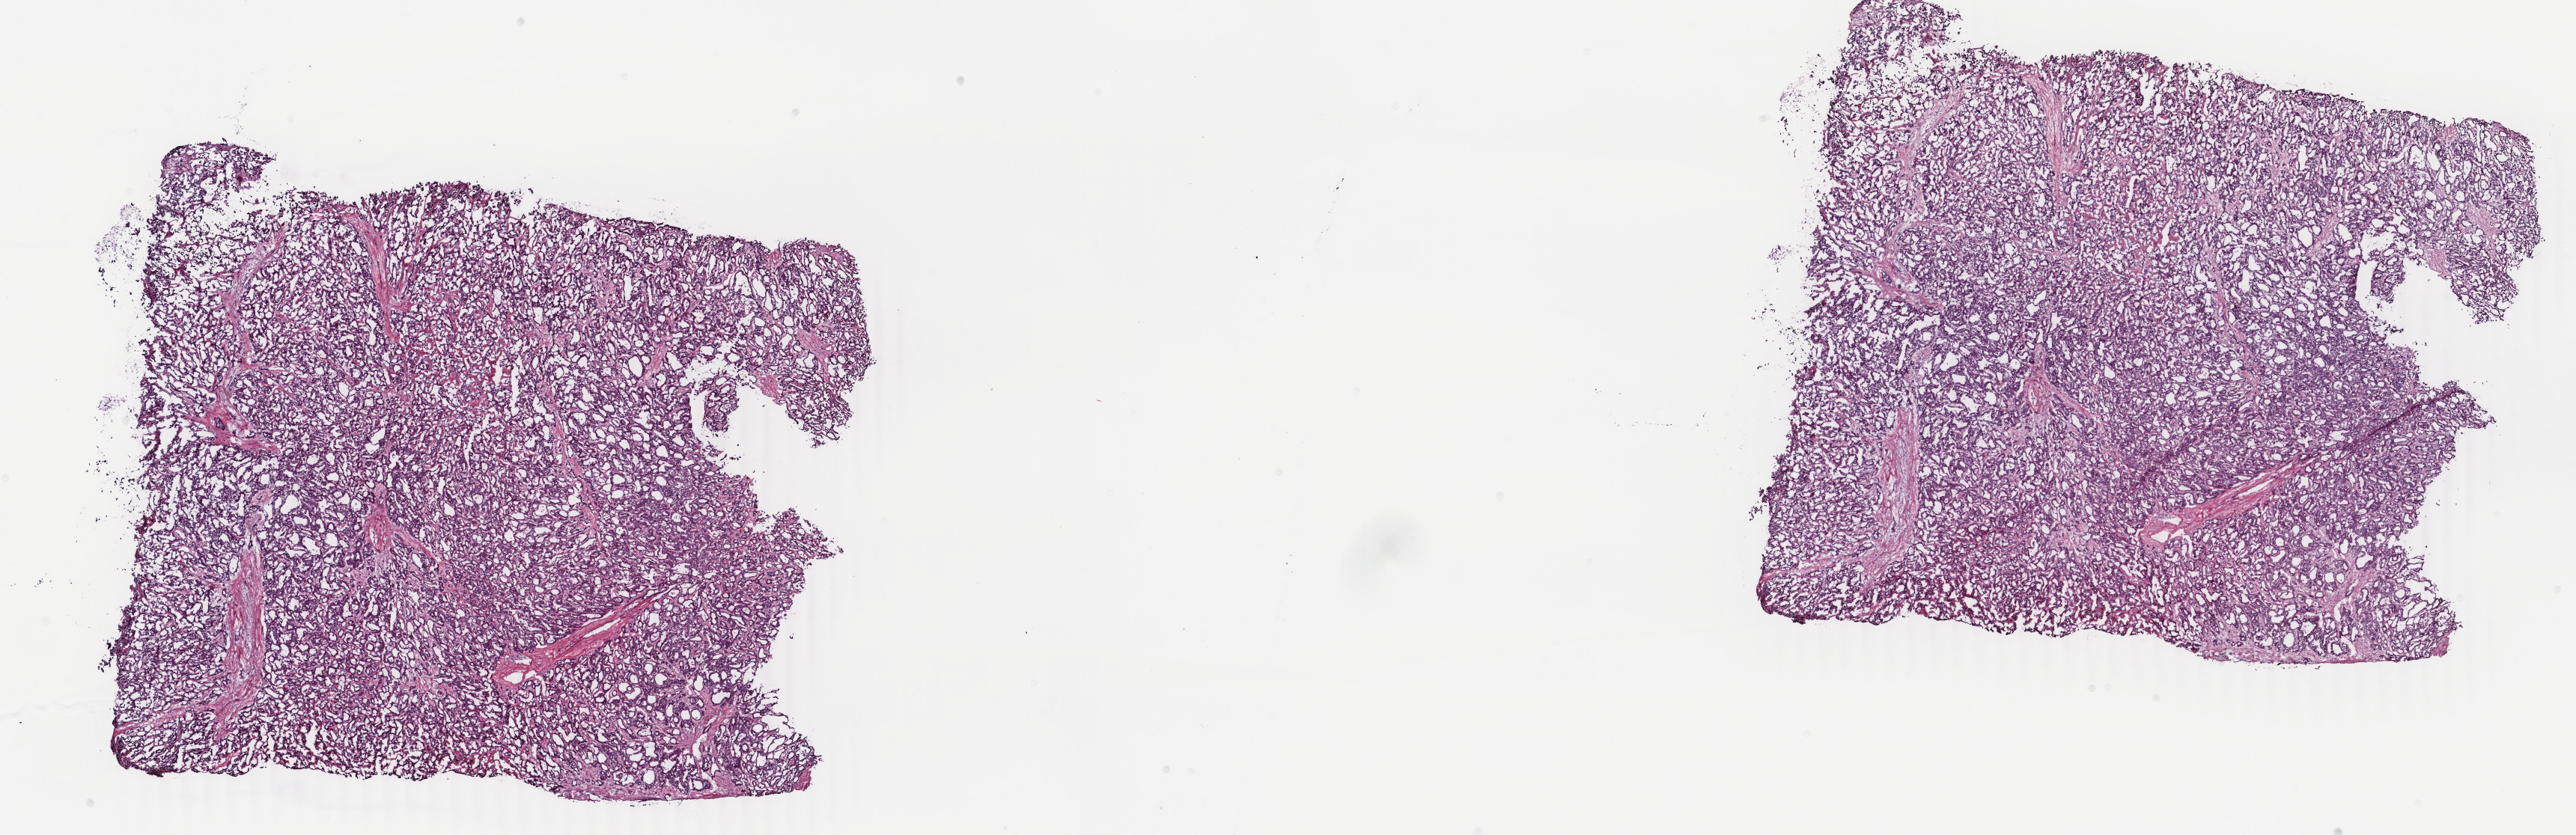
Whole-slide histology image, Hematoxylin and eosin (H&E) stained — low-resolution overview of the scanned area, about 27.4 x 8.9 mm (slide scanned at 40x), frozen section from the bottom of the tissue portion, primary tumour sample from the liver. Patient: female, age at initial diagnosis 72 years. Slide review estimates, as recorded: tumour cells 97%, tumour nuclei 90%, normal cells 0%, stromal cells 3%, necrosis 0%. Inflammatory infiltration, as recorded: lymphocyte infiltration 0%, monocyte infiltration 0%, neutrophil infiltration 0%.
• diagnosis: Hepatocellular carcinoma, NOS